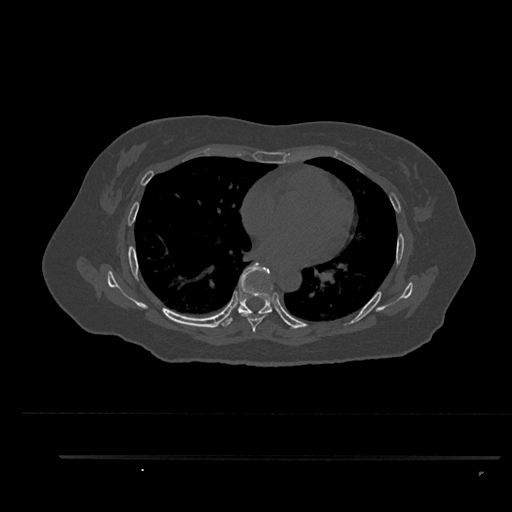
CT including the spine, one axial slice; slice 532 of 797 in the series (ordered by position); reconstruction kernel Br40s/3; 120 kVp; bone window (W 1800 / L 400 HU); 0.5 mm slice thickness; 512 × 512 image matrix, field of view 408 × 408 mm. Patient: female, 44 years. Case-level facts recorded for this patient, not image findings: primary cancer: renal; vertebrae with lytic lesions (as recorded): L1.
Outlined on this slice (semi-automatically segmented with operator editing):
- T6 vertebra: bounding box <241,312,271,333> (left, top, right, bottom; pixels)
- T7 vertebra: <222,262,273,327>